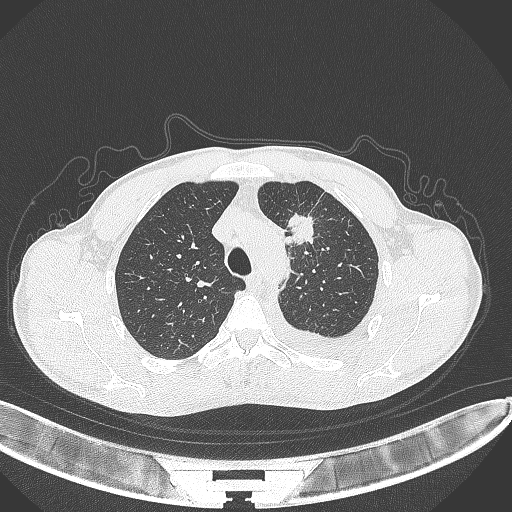
Chest CT, one axial slice; slice 264 of 371 in the series (ordered by position); reconstruction kernel B70f; lung window (W 1500 / L -600 HU); 1 mm slice thickness; 512 × 512 image matrix, field of view 400 × 400 mm. Patient: male, 49 years. From the clinical record (not read from this slice): clinical TNM (as recorded): T1c N1 M1.
Structures marked on this image (bounding box drawn by a radiologist):
- lung tumour (recorded histology: adenocarcinoma): box from (x=287, y=207) to (x=320, y=254) px